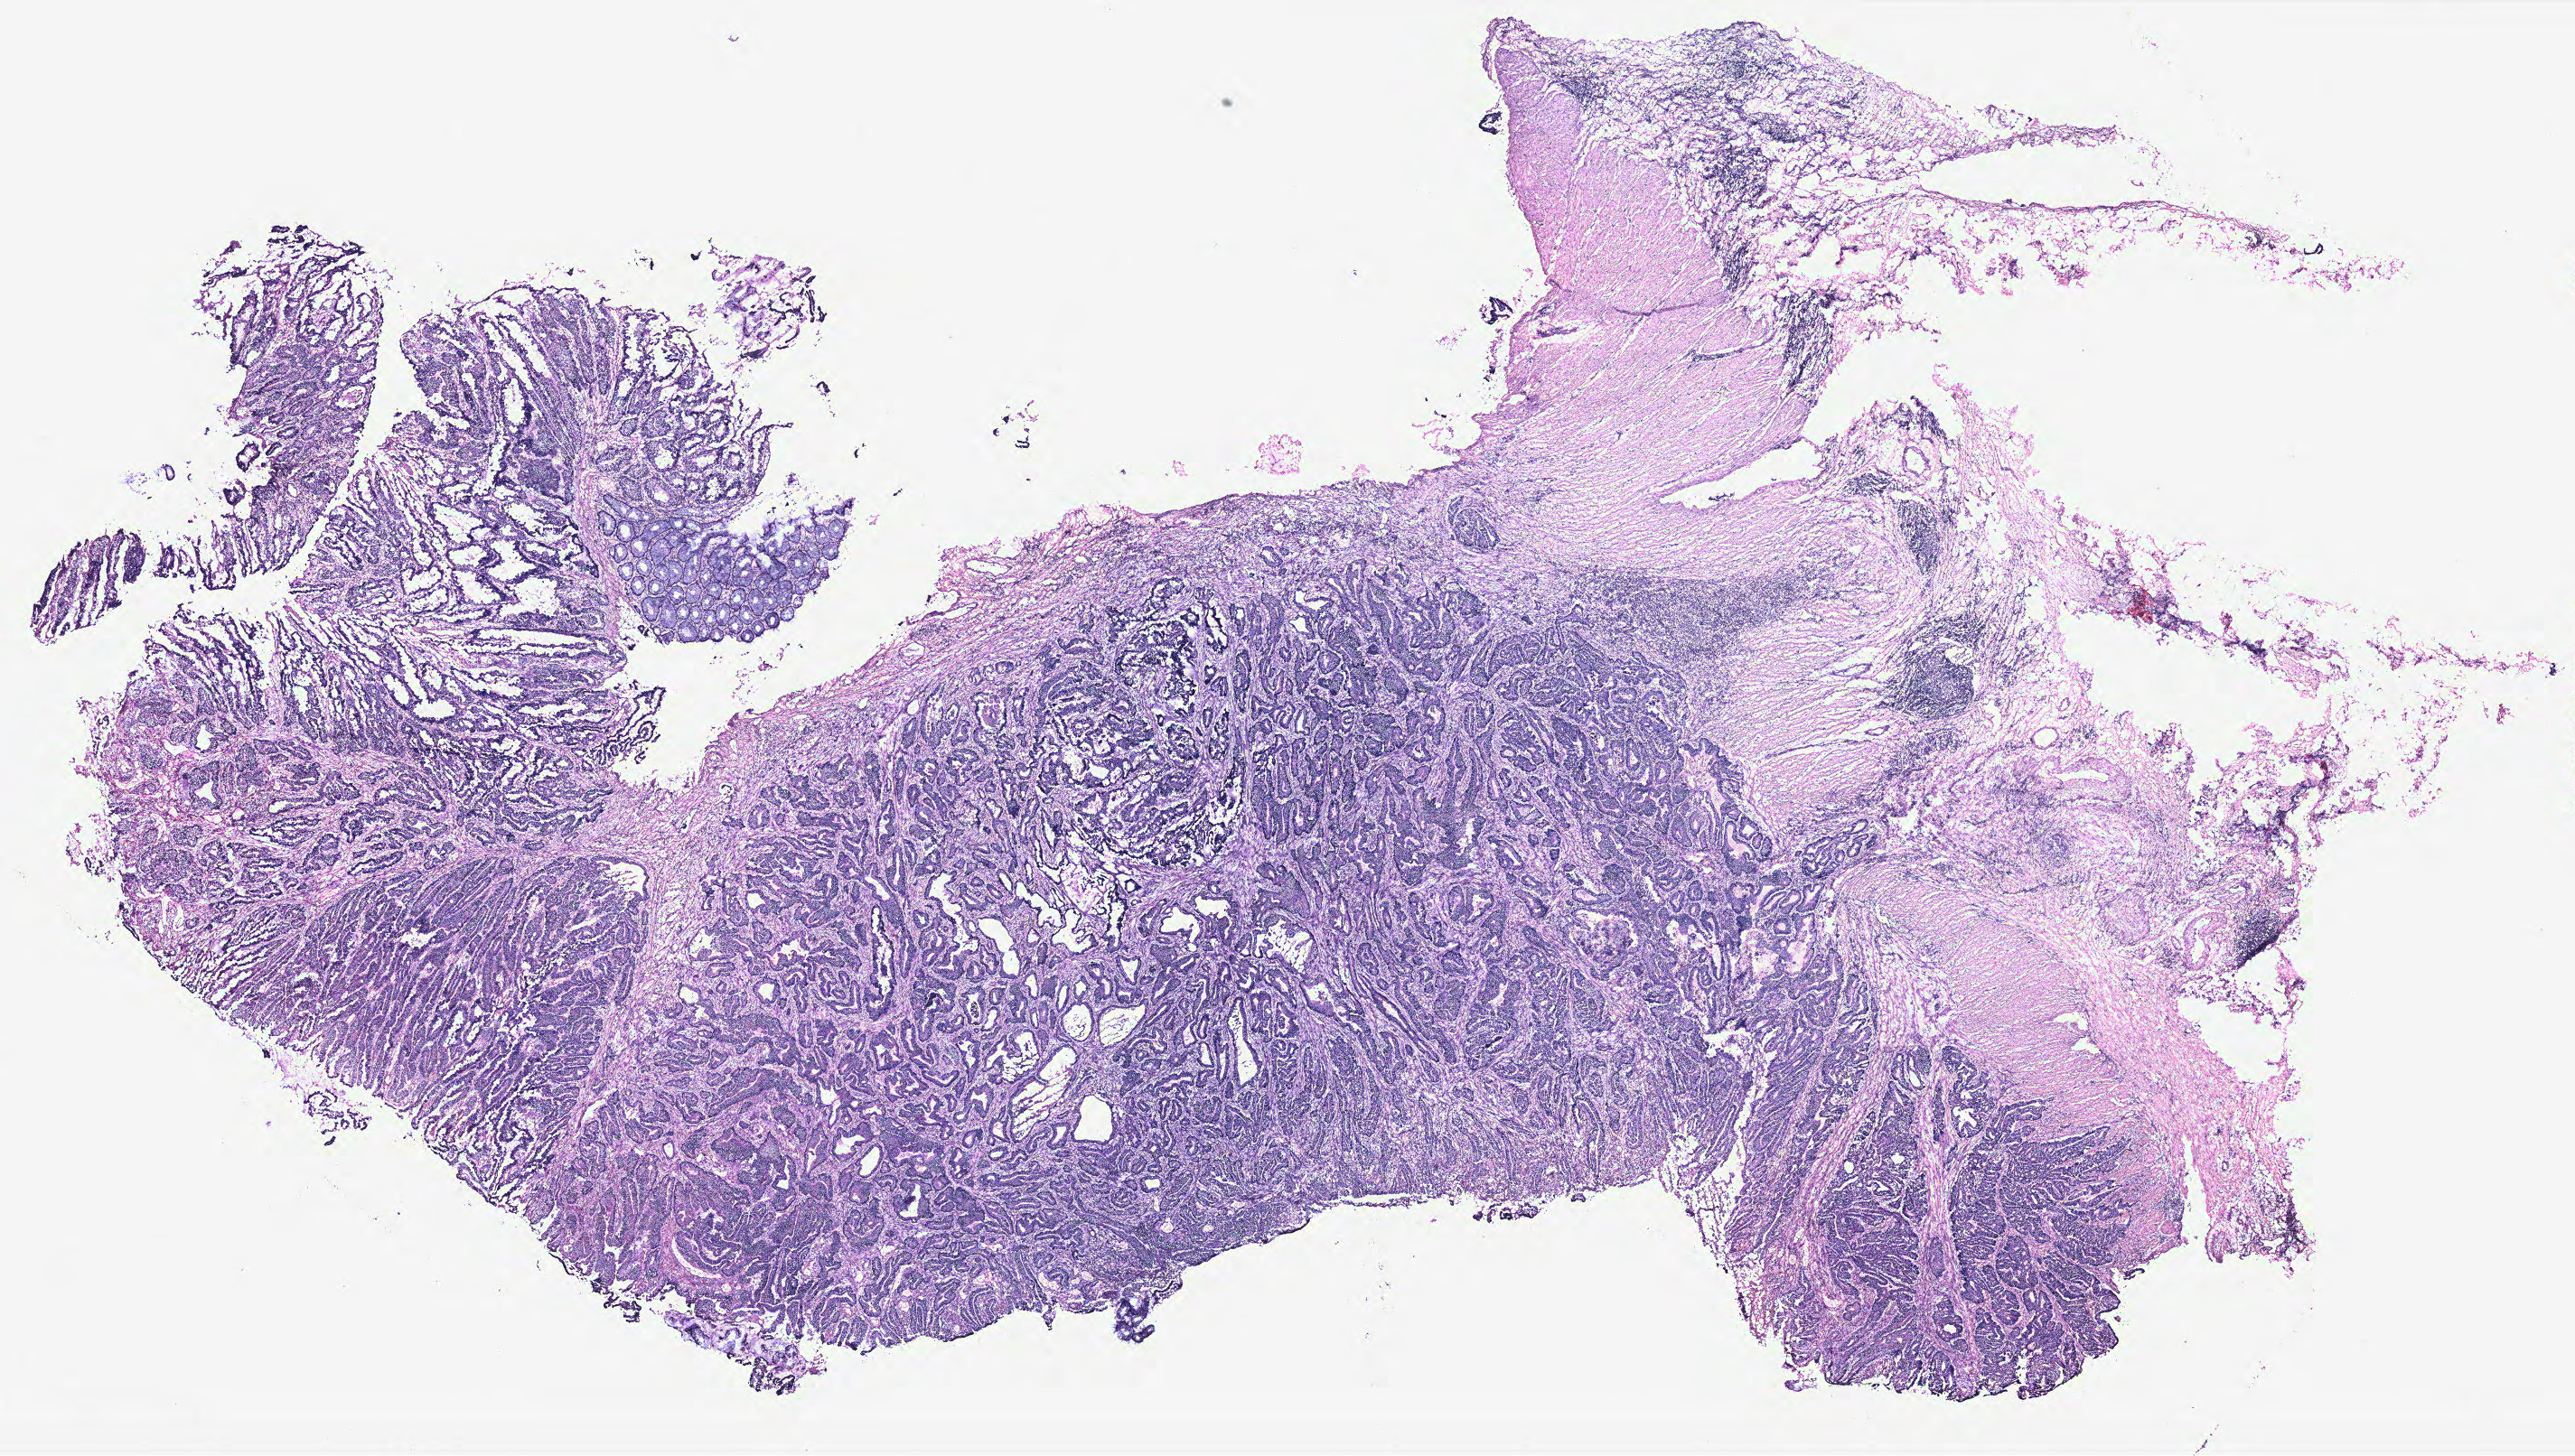
H&E whole-slide image — a low-resolution overview of the entire scanned area, about 22.8 x 12.9 mm (from a 40x scan). Tumour tissue sample, colon. Female, 55 y/o.
Diagnosis: Adenocarcinoma, NOS.